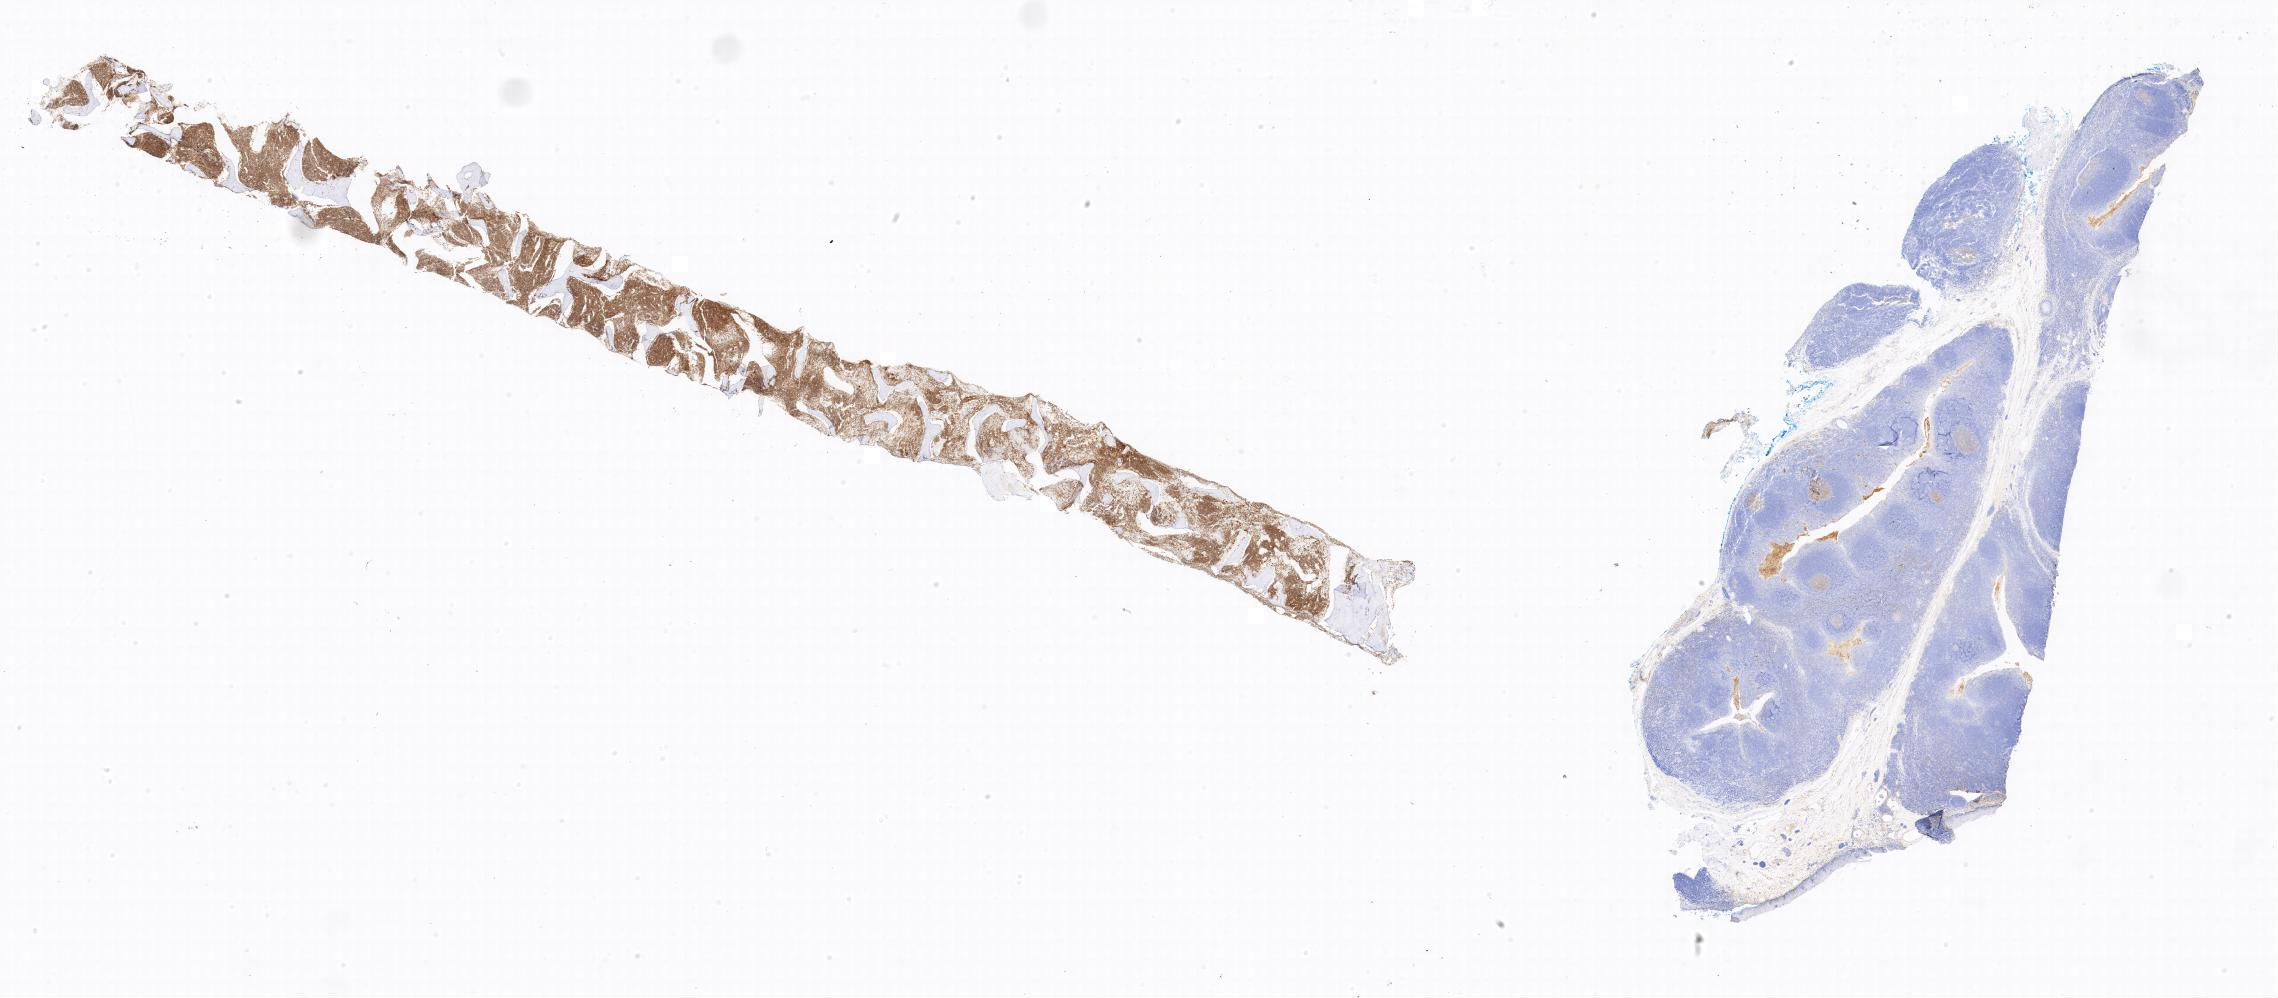
IHC for CD10, whole-slide image — low-resolution overview of the scanned area, specimen: tumor tissue, site: bone marrow. Patient: male, aged 18.
Histologic diagnosis: Burkitt lymphoma, NOS.